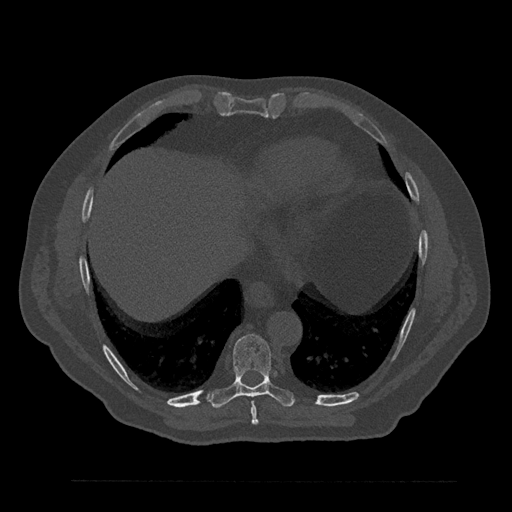
CT including the spine, one axial slice. Reconstruction kernel Br40s/3. 120 kVp. Bone window (W 1800 / L 400 HU). 0.5 mm slice thickness. 512 × 512 image matrix, field of view 430 × 430 mm. Male patient, age 61 years. From the clinical record (not read from this slice): primary cancer: prostate.
Outlined on this slice (semi-automatic segmentation, software-assisted and operator-edited):
- T8 vertebra: box from (x=251, y=401) to (x=259, y=425) px
- T9 vertebra: (x=208, y=334)–(x=295, y=408)